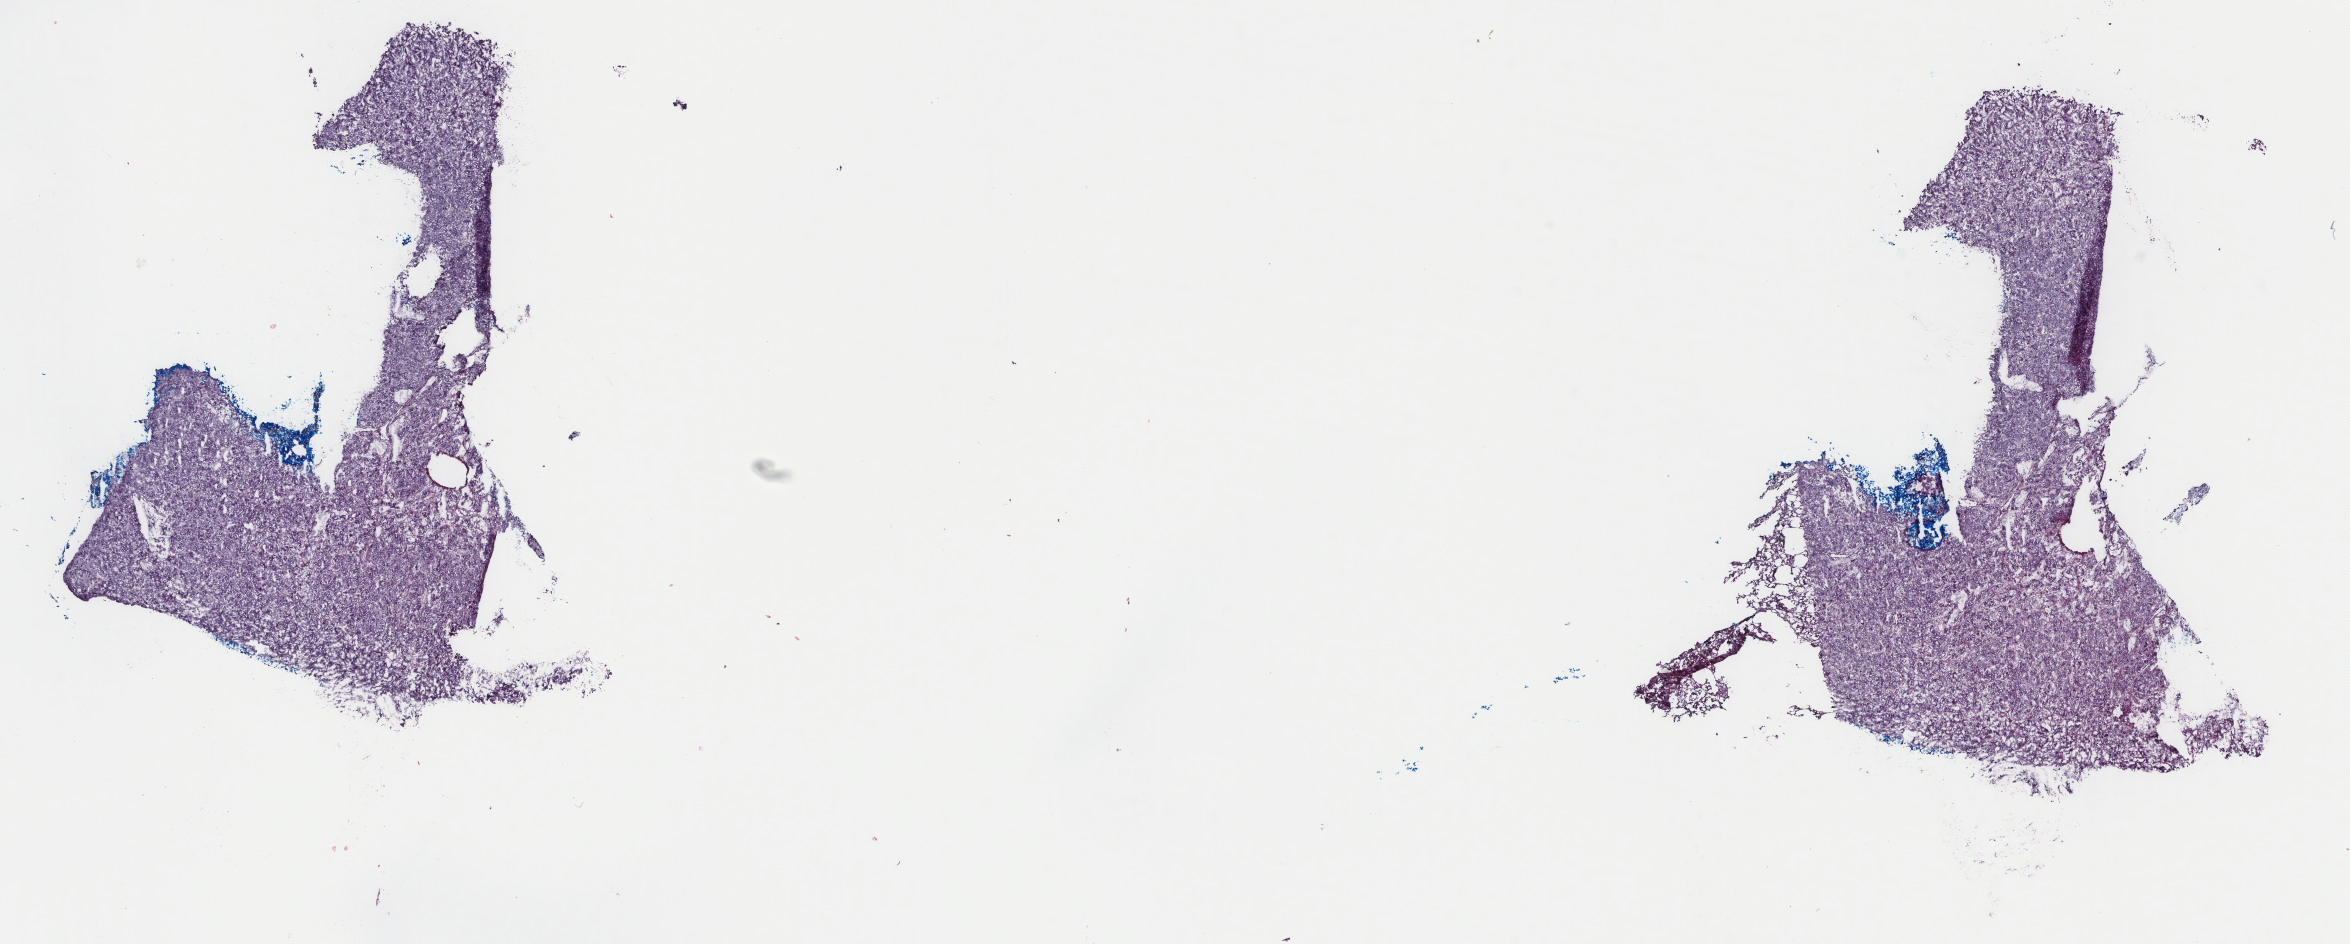
Digitized Hematoxylin and eosin (H&E) stained tissue section (whole slide), low-resolution overview of the scanned area, about 18.7 x 7.5 mm (slide scanned at 40x); frozen section from the top of the tissue portion; primary tumour sample from the liver. Female patient; age at initial diagnosis 38 years. Slide review estimates, as recorded: tumour cells 100%, tumour nuclei 92%.
Histologic diagnosis: Hepatocellular carcinoma, NOS.